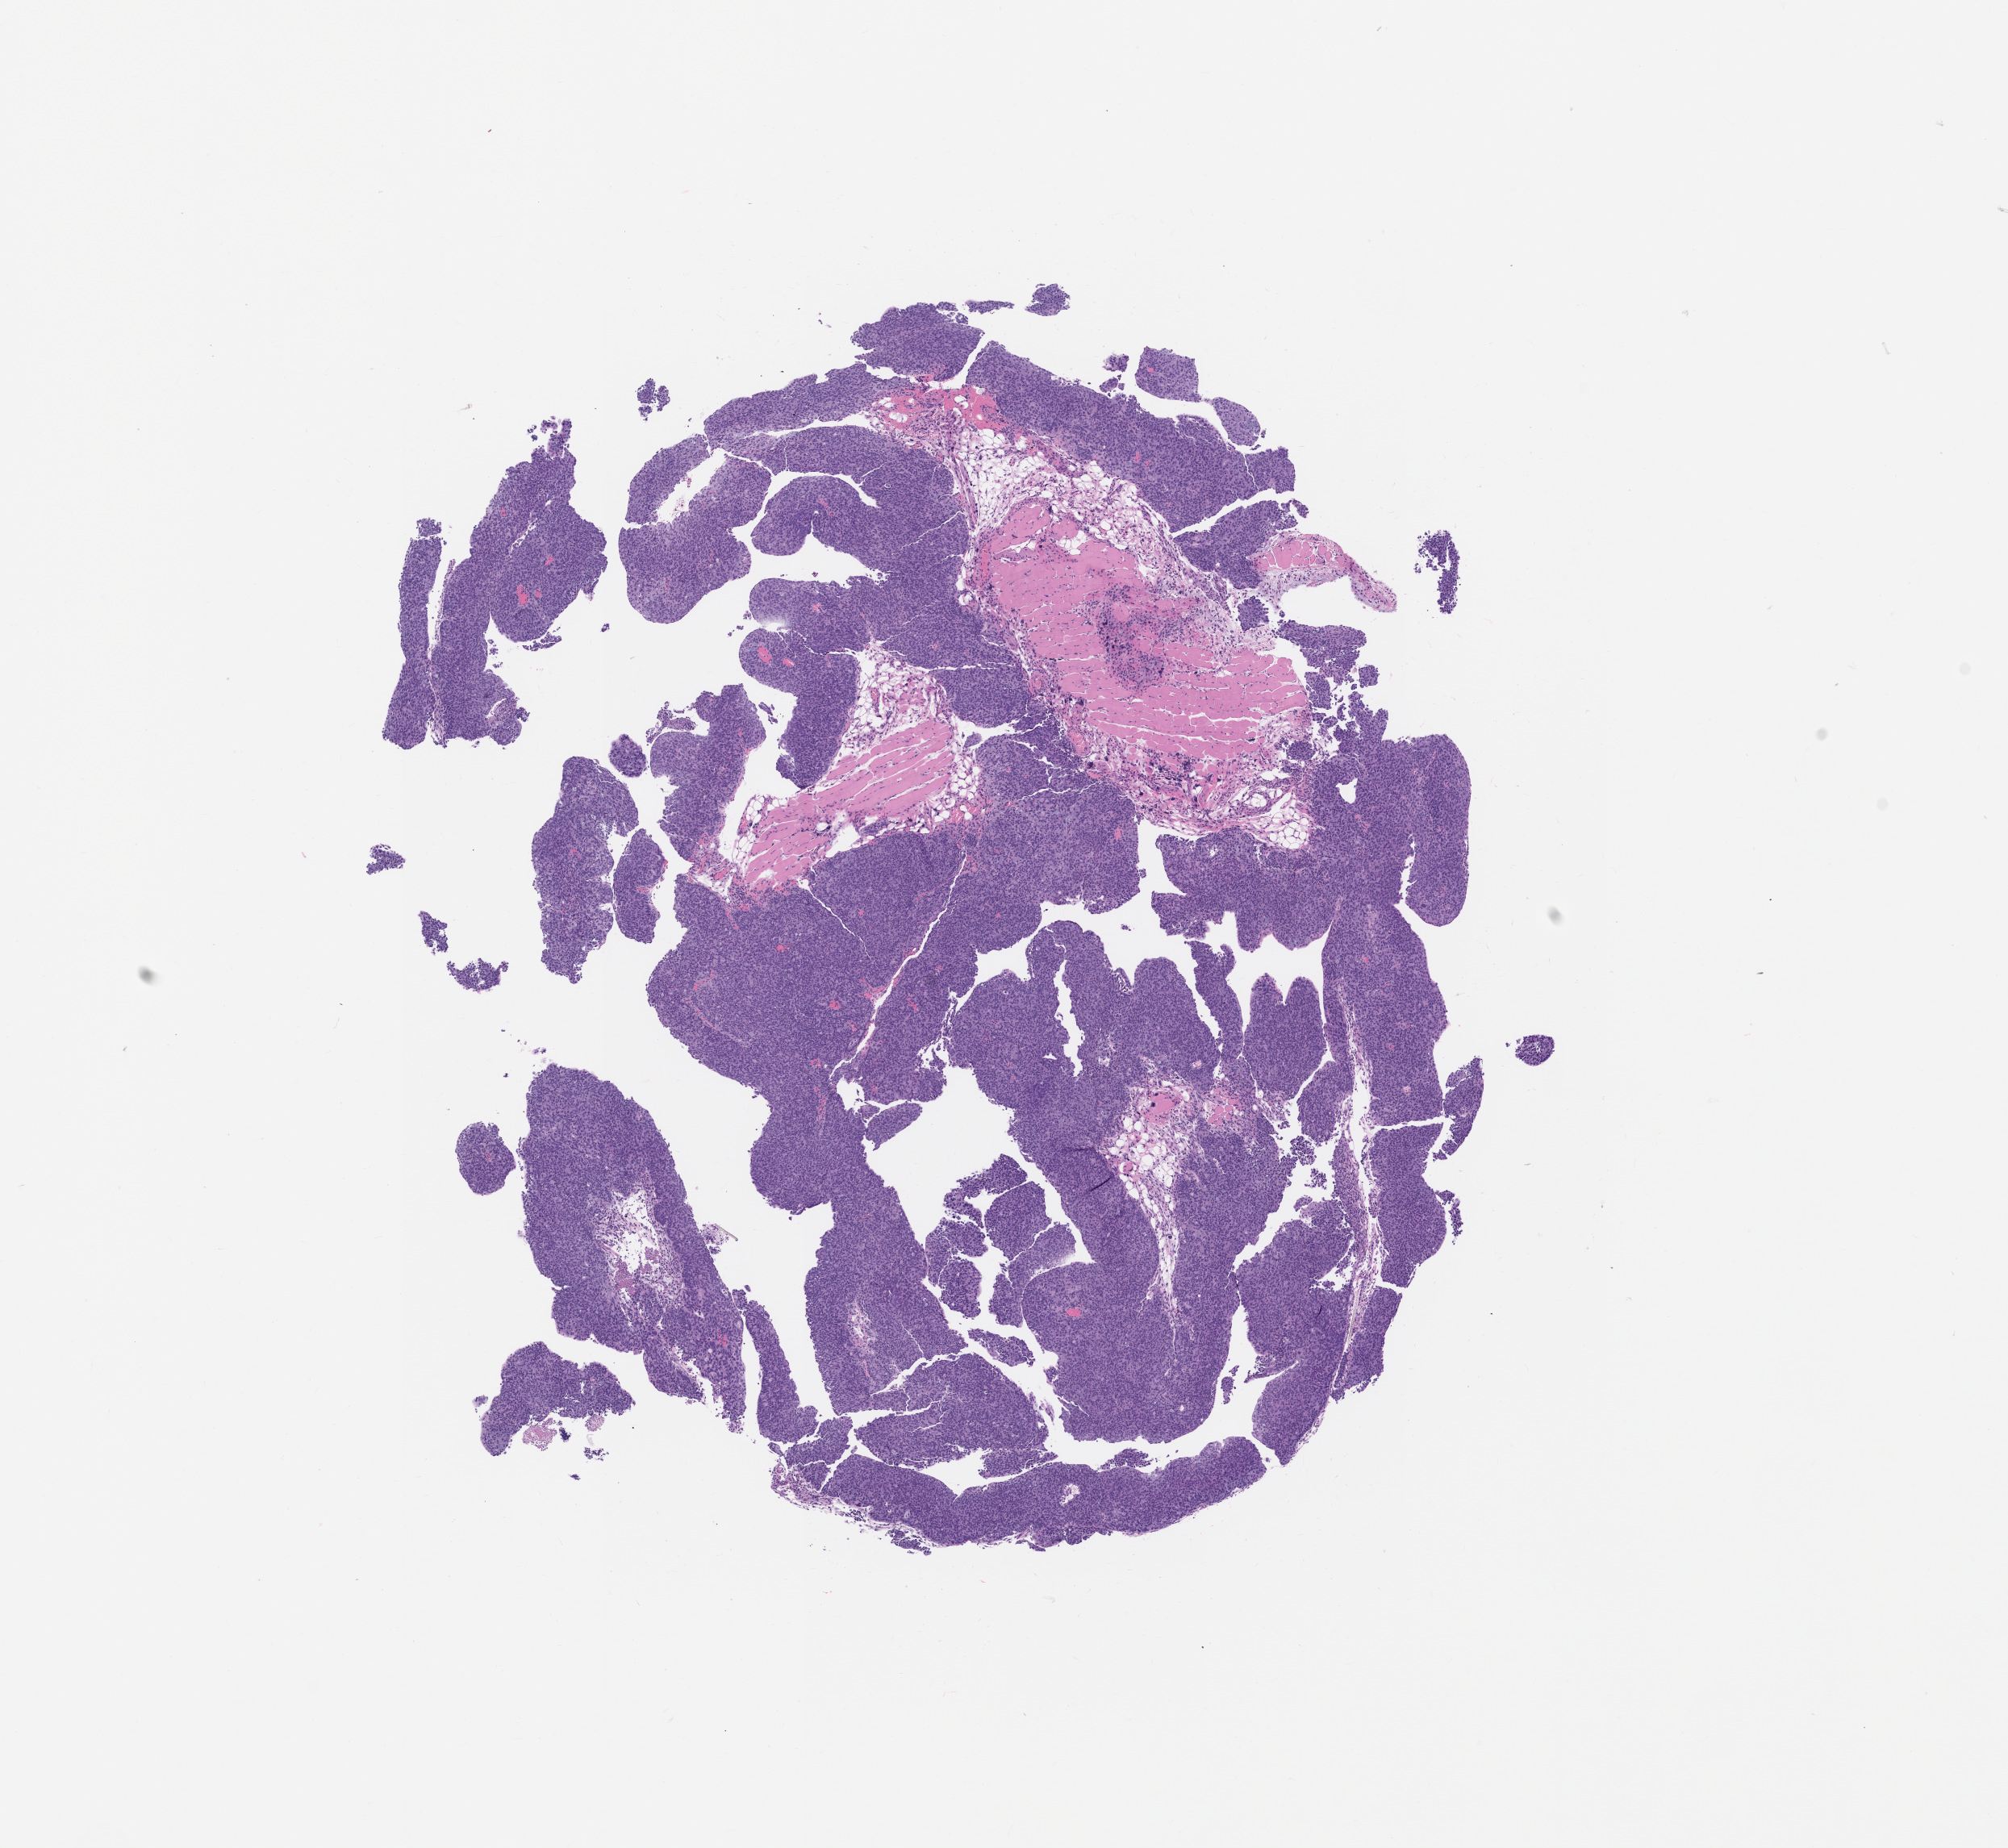
Haematoxylin and eosin whole-slide image of a patient-derived xenograft (PDX) tumor grown in a mouse, passage 2, a low-resolution overview of the entire scanned area, about 10.0 x 9.2 mm. Formalin-fixed, paraffin-embedded (FFPE) tissue. Originating tumor site category: gastrointestinal tract.
Originating patient diagnosis: Gastric Adenocarcinoma.